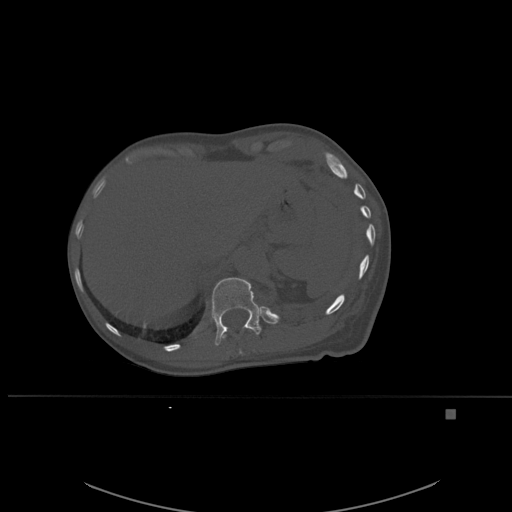
CT including the spine, one axial slice. Position 285 of 537 along the scan axis. Bone window (W 1800 / L 400 HU). 512 × 512 image matrix. Patient: female, 45 years. From the clinical record (not read from this slice): primary cancer: lung.
Annotated regions visible in this slice (semi-automatically segmented with operator editing):
- T11 vertebra: bounding box <220,328,252,355> (left, top, right, bottom; pixels)
- T12 vertebra: <211,277,262,346>